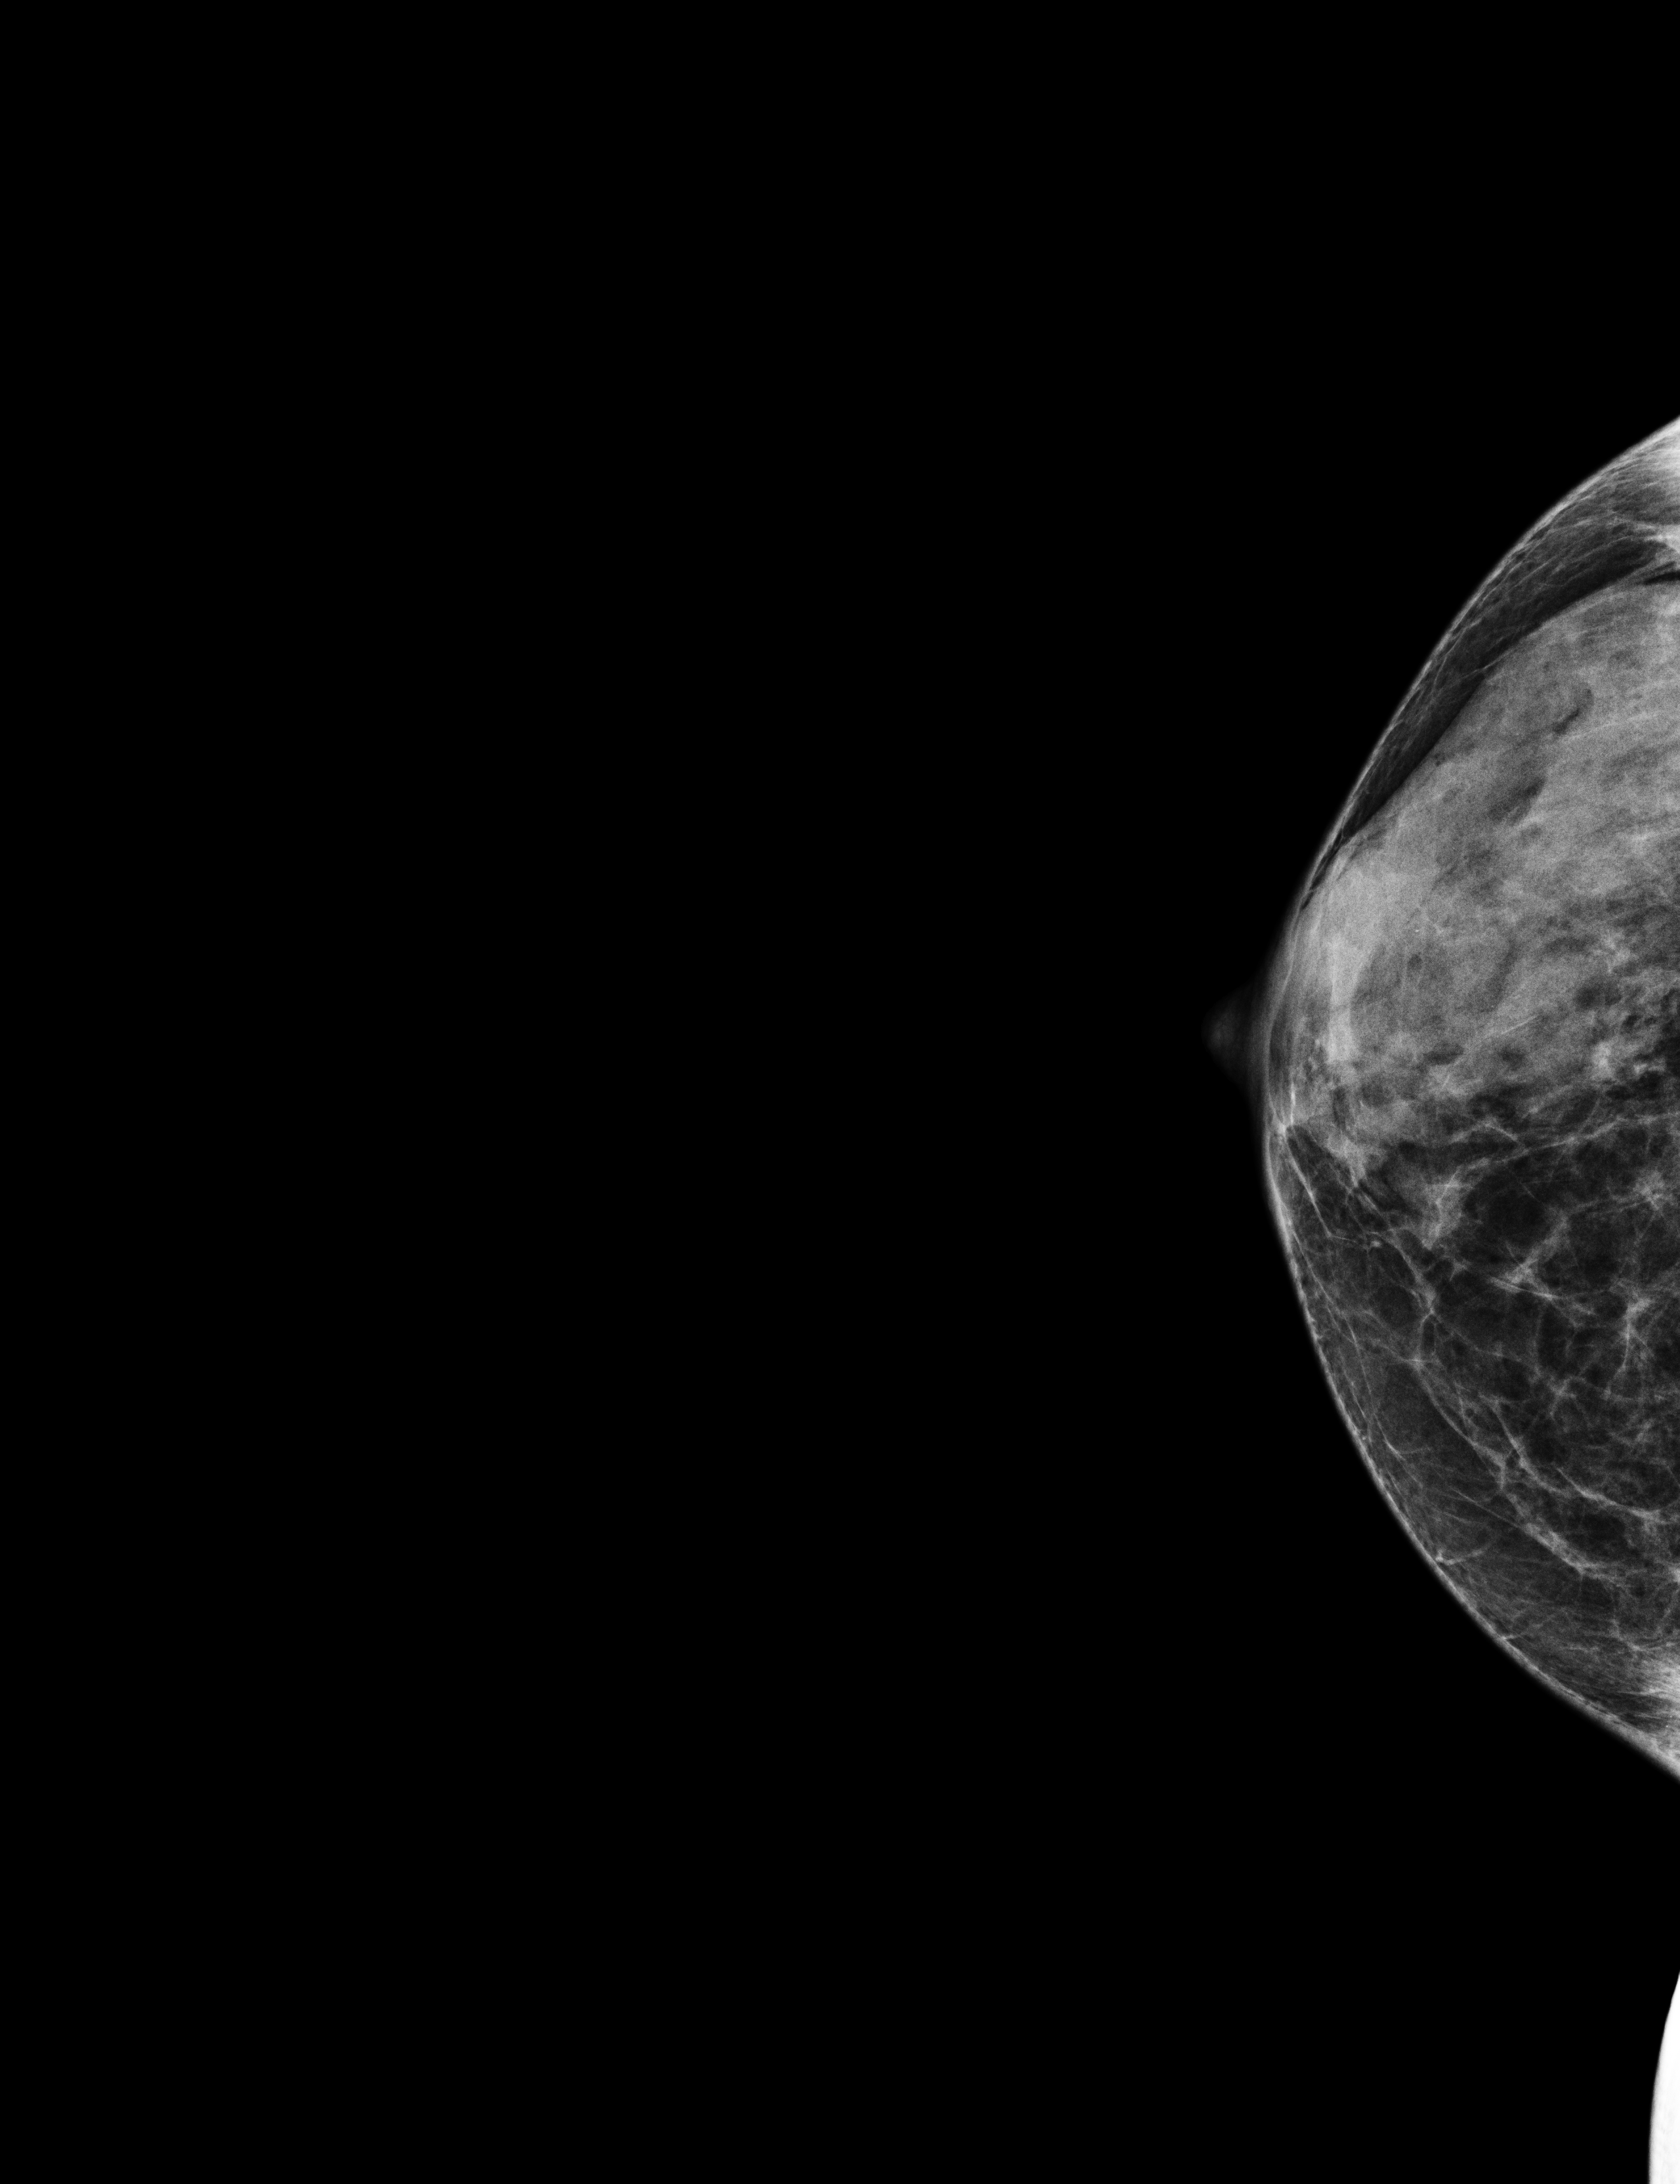
Screening examination. Patient aged 61 years (female).
Image type: full-field digital mammogram. Breast: right. Projection: CC view.